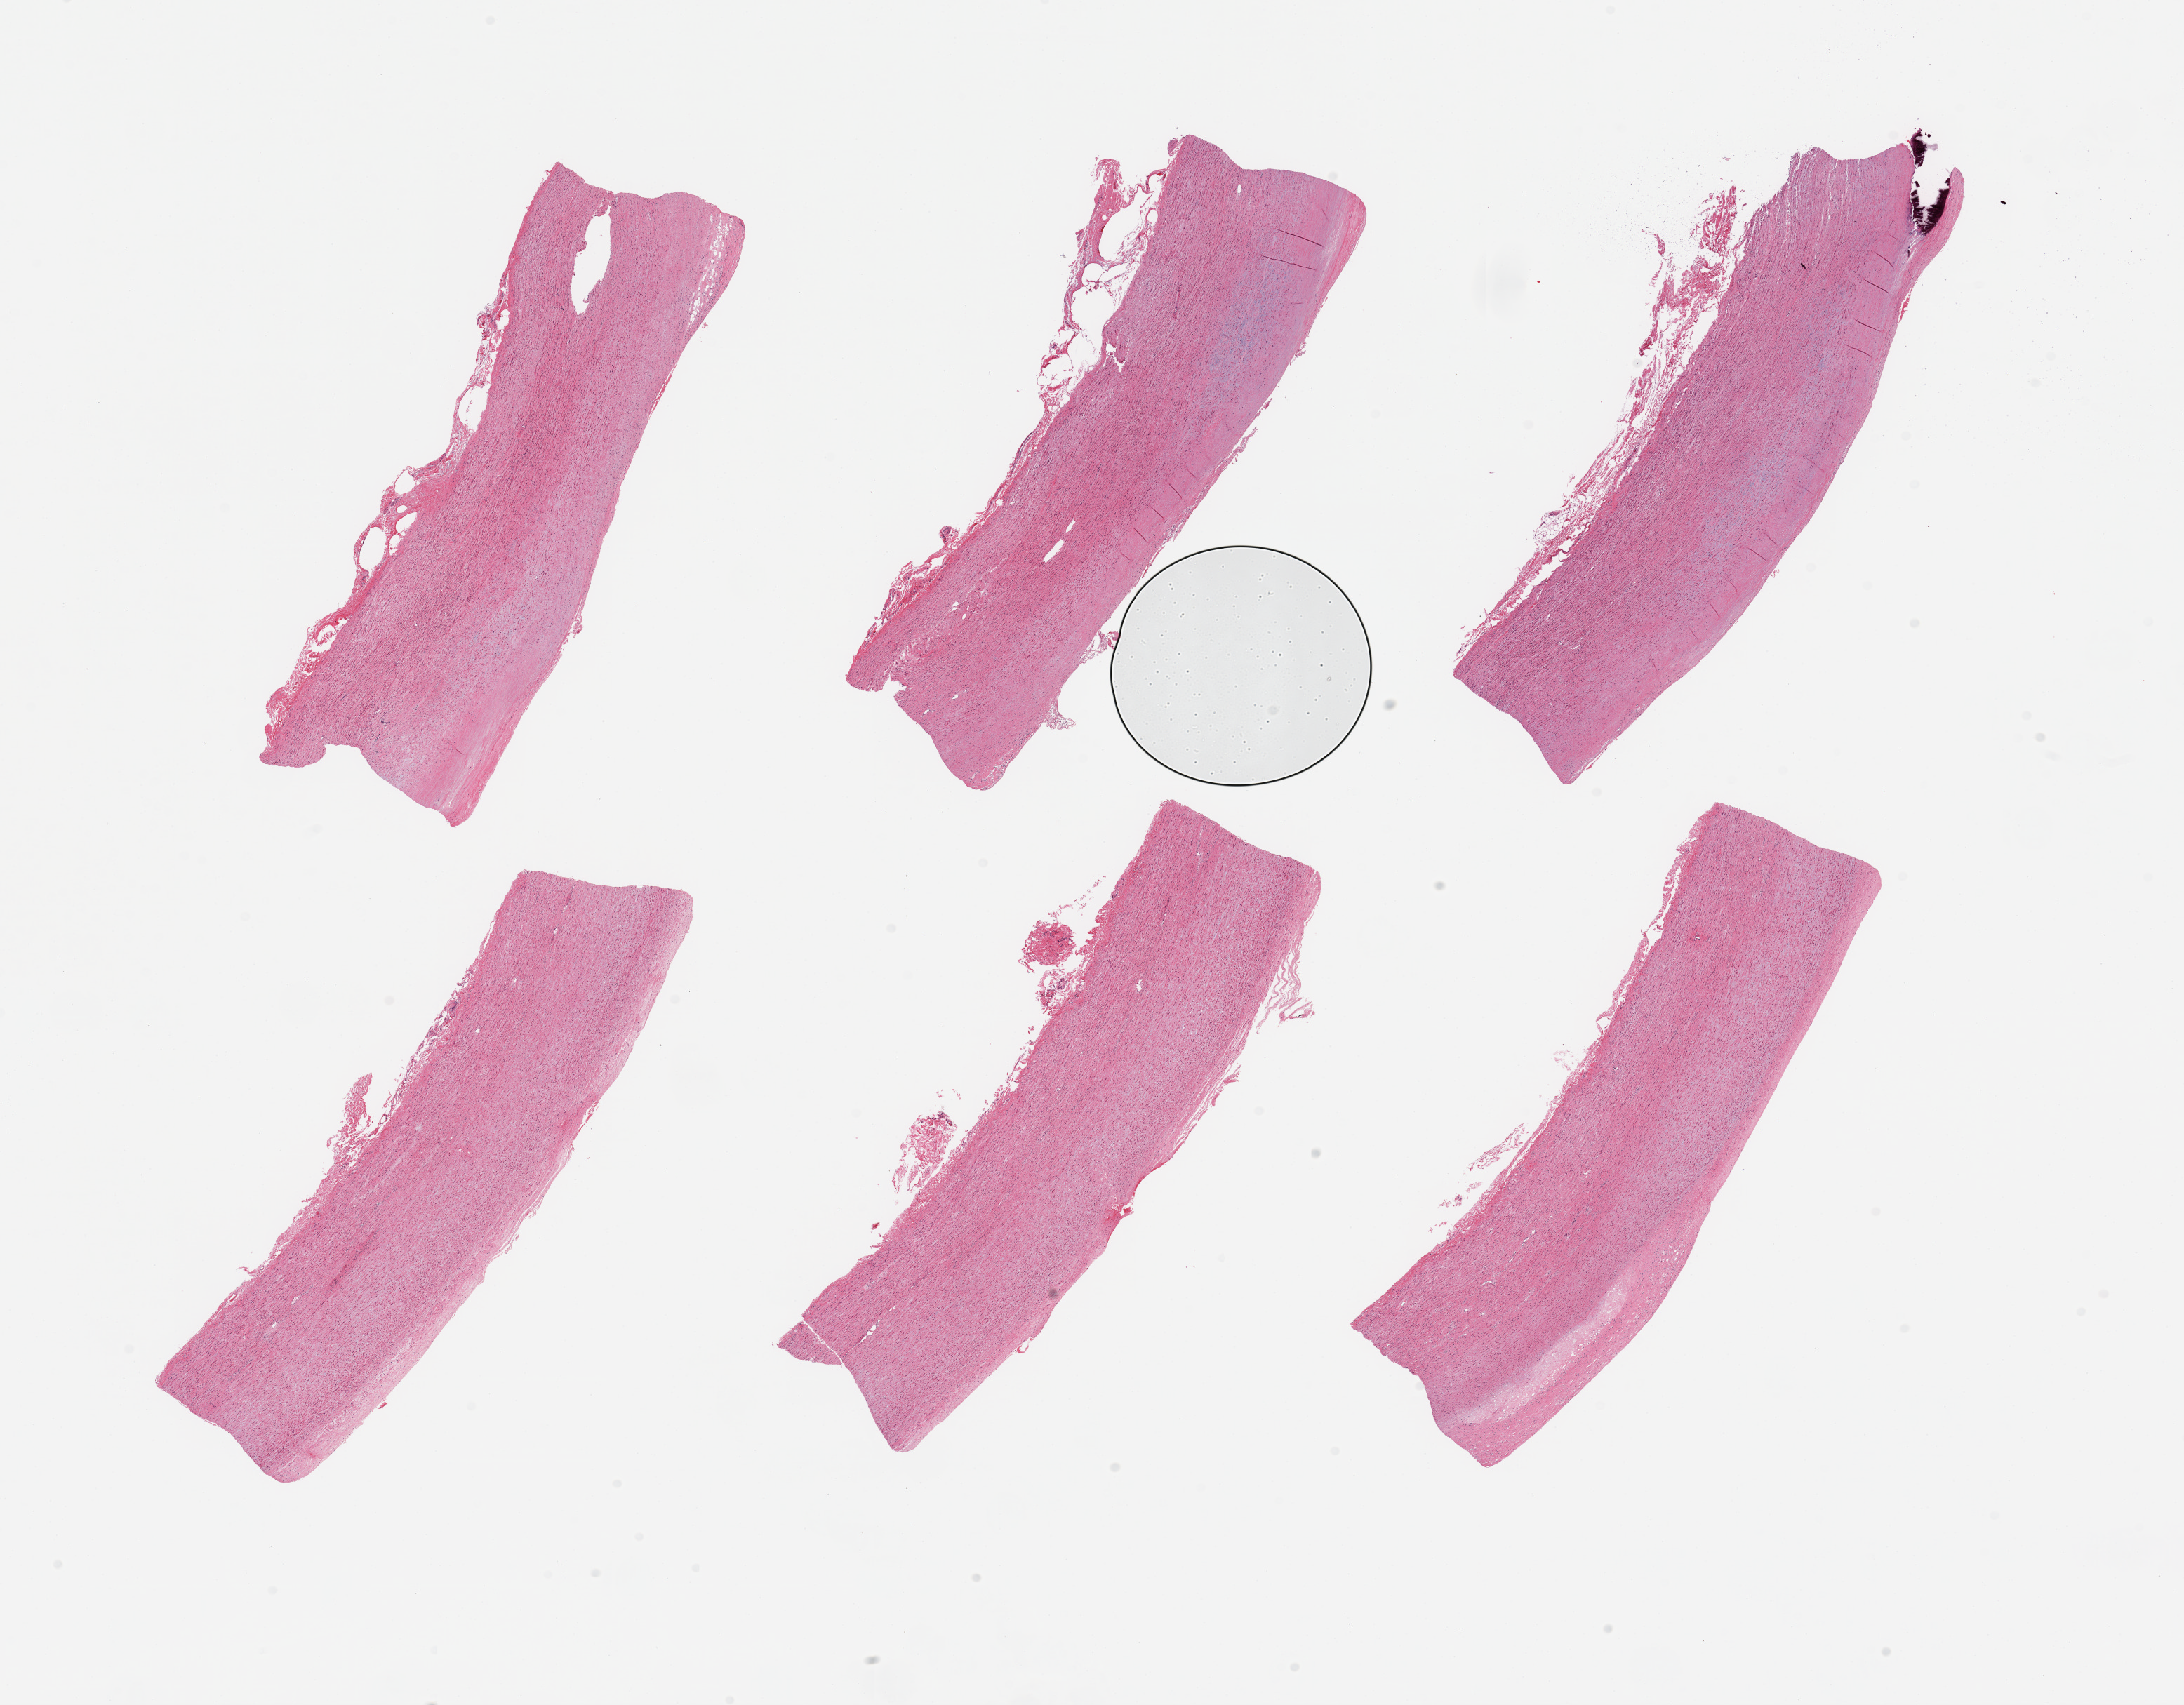
Digitized H&E-stained section — low-resolution overview of the scanned area, about 24.6 x 19.2 mm. PAXgene-fixed paraffin-embedded (PFPE) section. Target tissue: aorta. Tissue donor sample. Male donor.
* pathologist's review note for this sample: 6 pieces, atherosis up to ~0.8mm, focally calcified